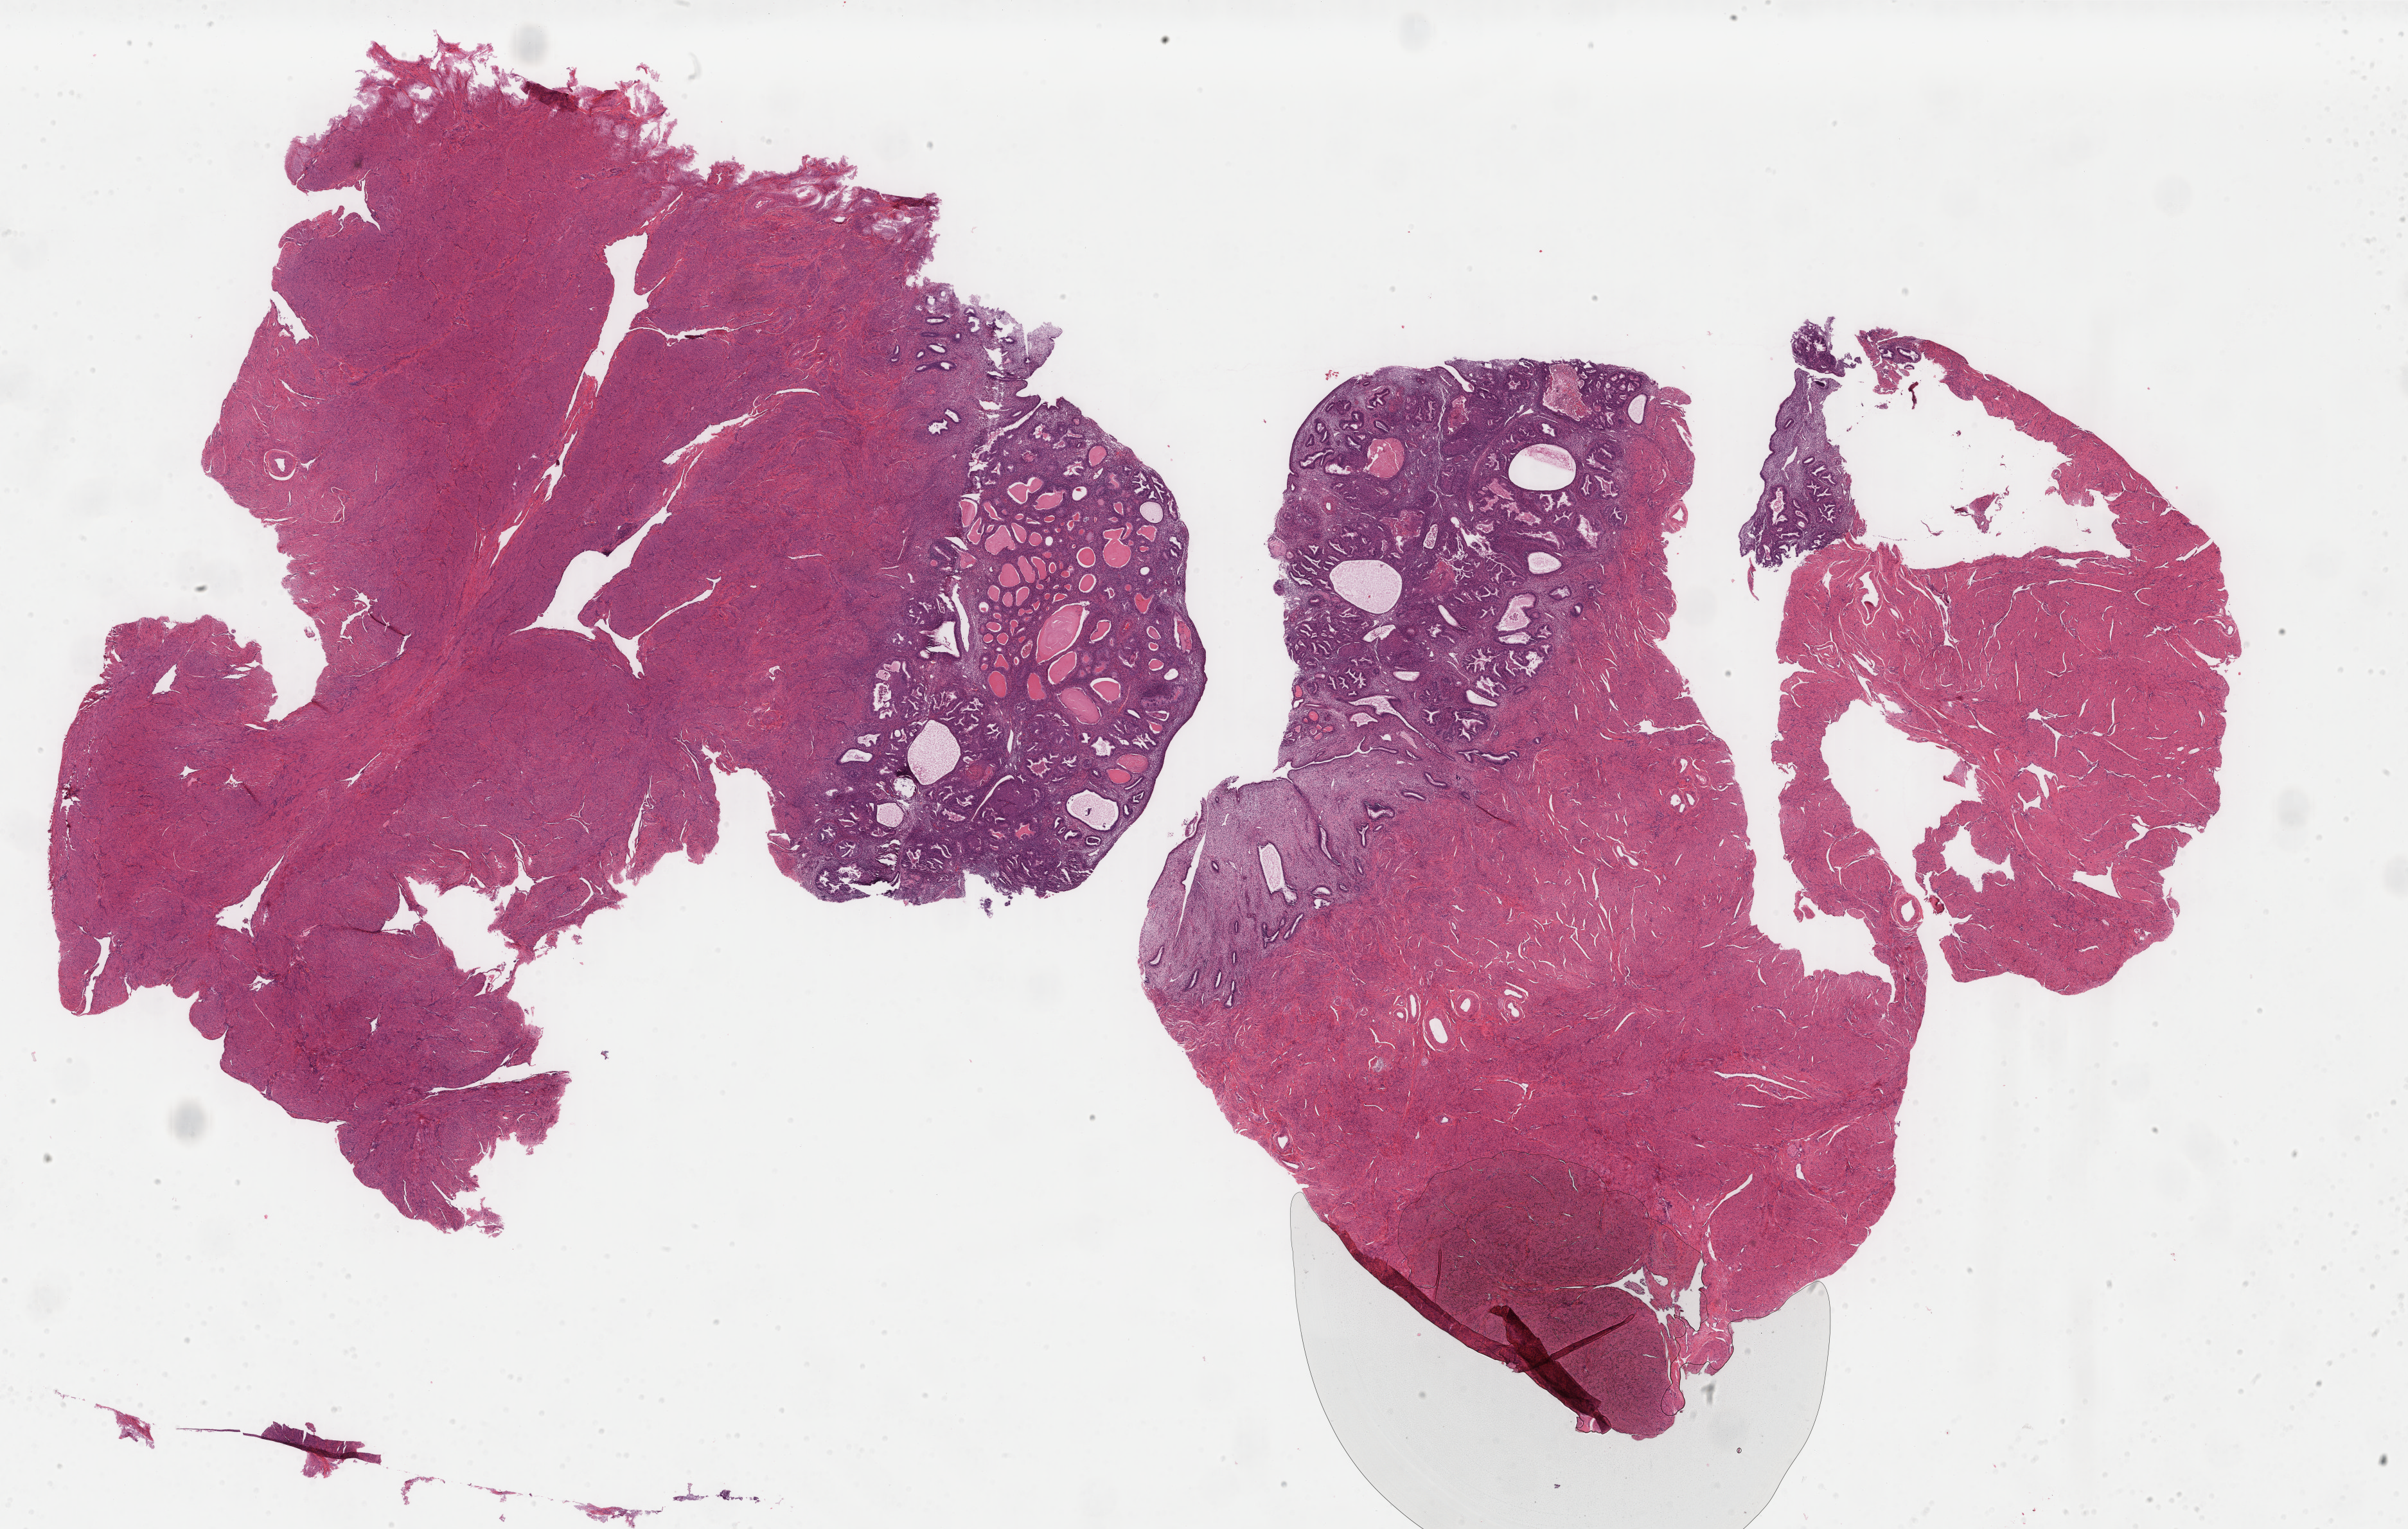
Digitized H&E tissue section (whole slide) — shown as a low-resolution overview of the whole scanned area (about 29.7 x 18.9 mm, from a 40x scan), formalin-fixed paraffin-embedded (FFPE) diagnostic section, primary tumour sample from the uterus. Patient: female, age at initial diagnosis 51 years. Histologic grade: G3 (poorly differentiated).
- pathologic diagnosis: Endometrioid adenocarcinoma, NOS (endometrium)
- lymph nodes positive (case pathology): 0 of 10 examined
- FIGO stage: IIIA